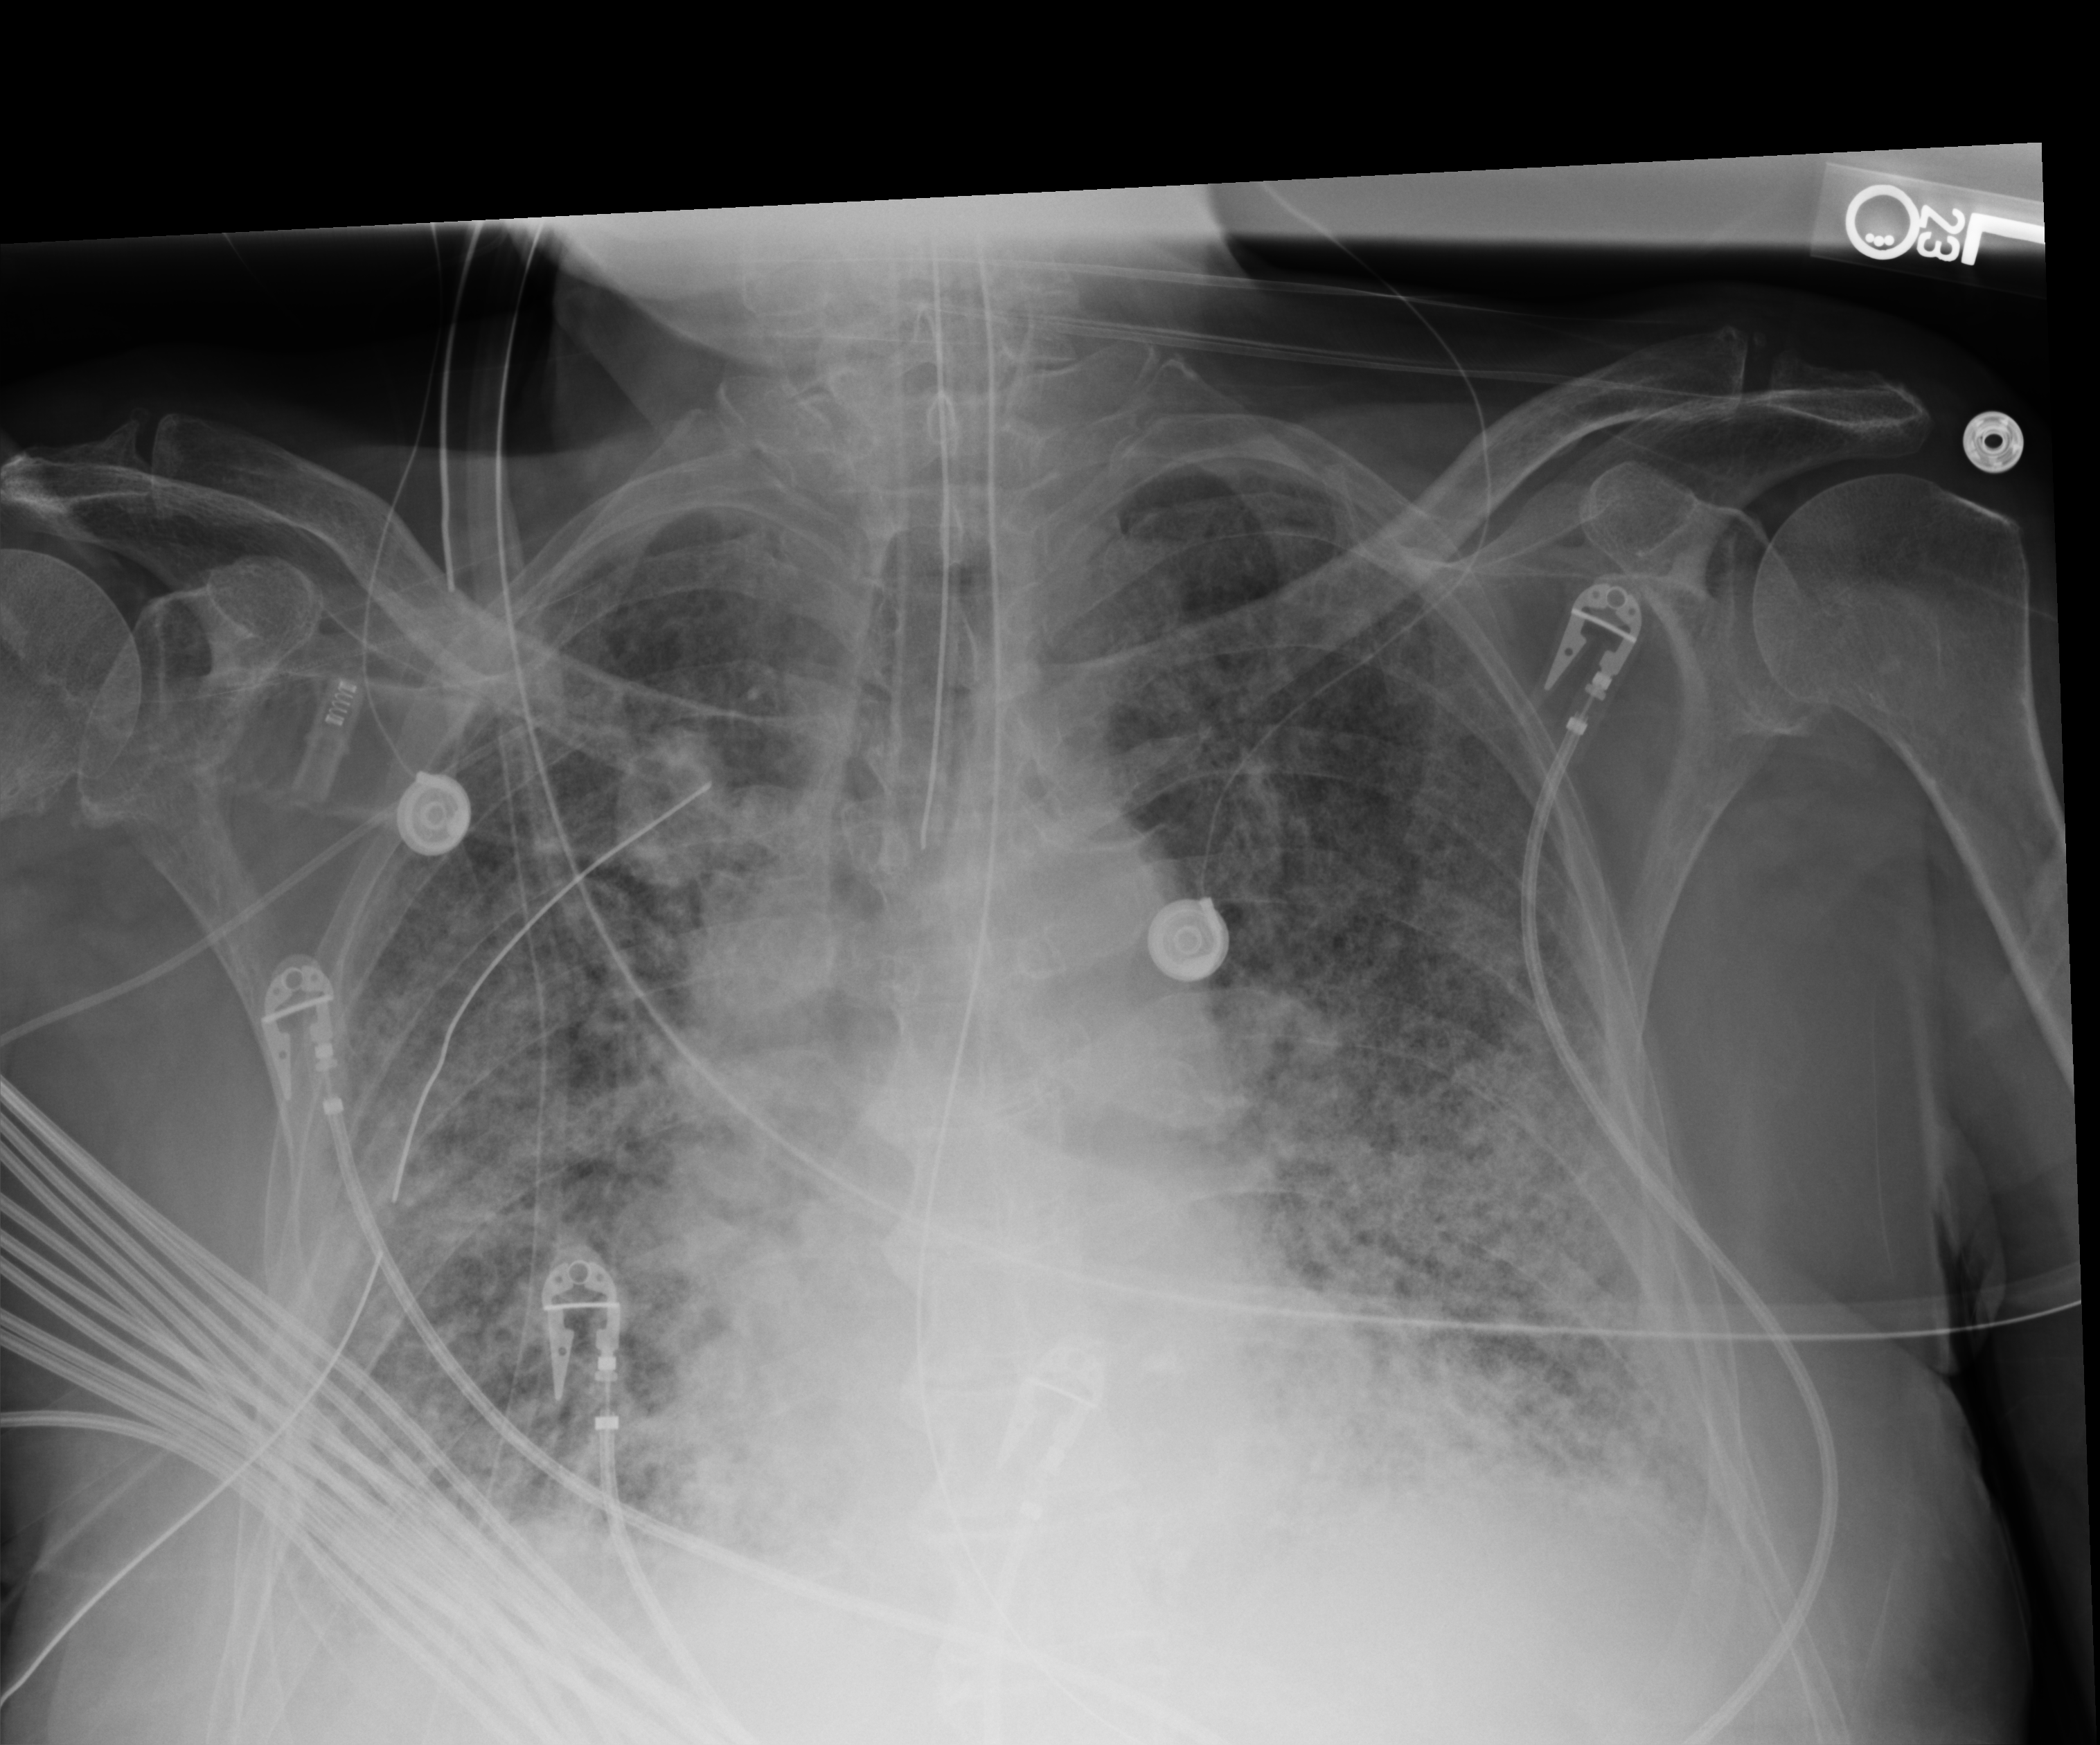
Portable chest radiograph, anteroposterior (AP) projection. Male patient hospitalised with COVID-19, age 75–90 years.
From the hospital-stay record, not from the radiograph (when in the stay this image was taken is not recorded): diabetes (admission record): no; admitted to intensive care during this hospital stay: yes; mechanically ventilated during this hospital stay: yes.